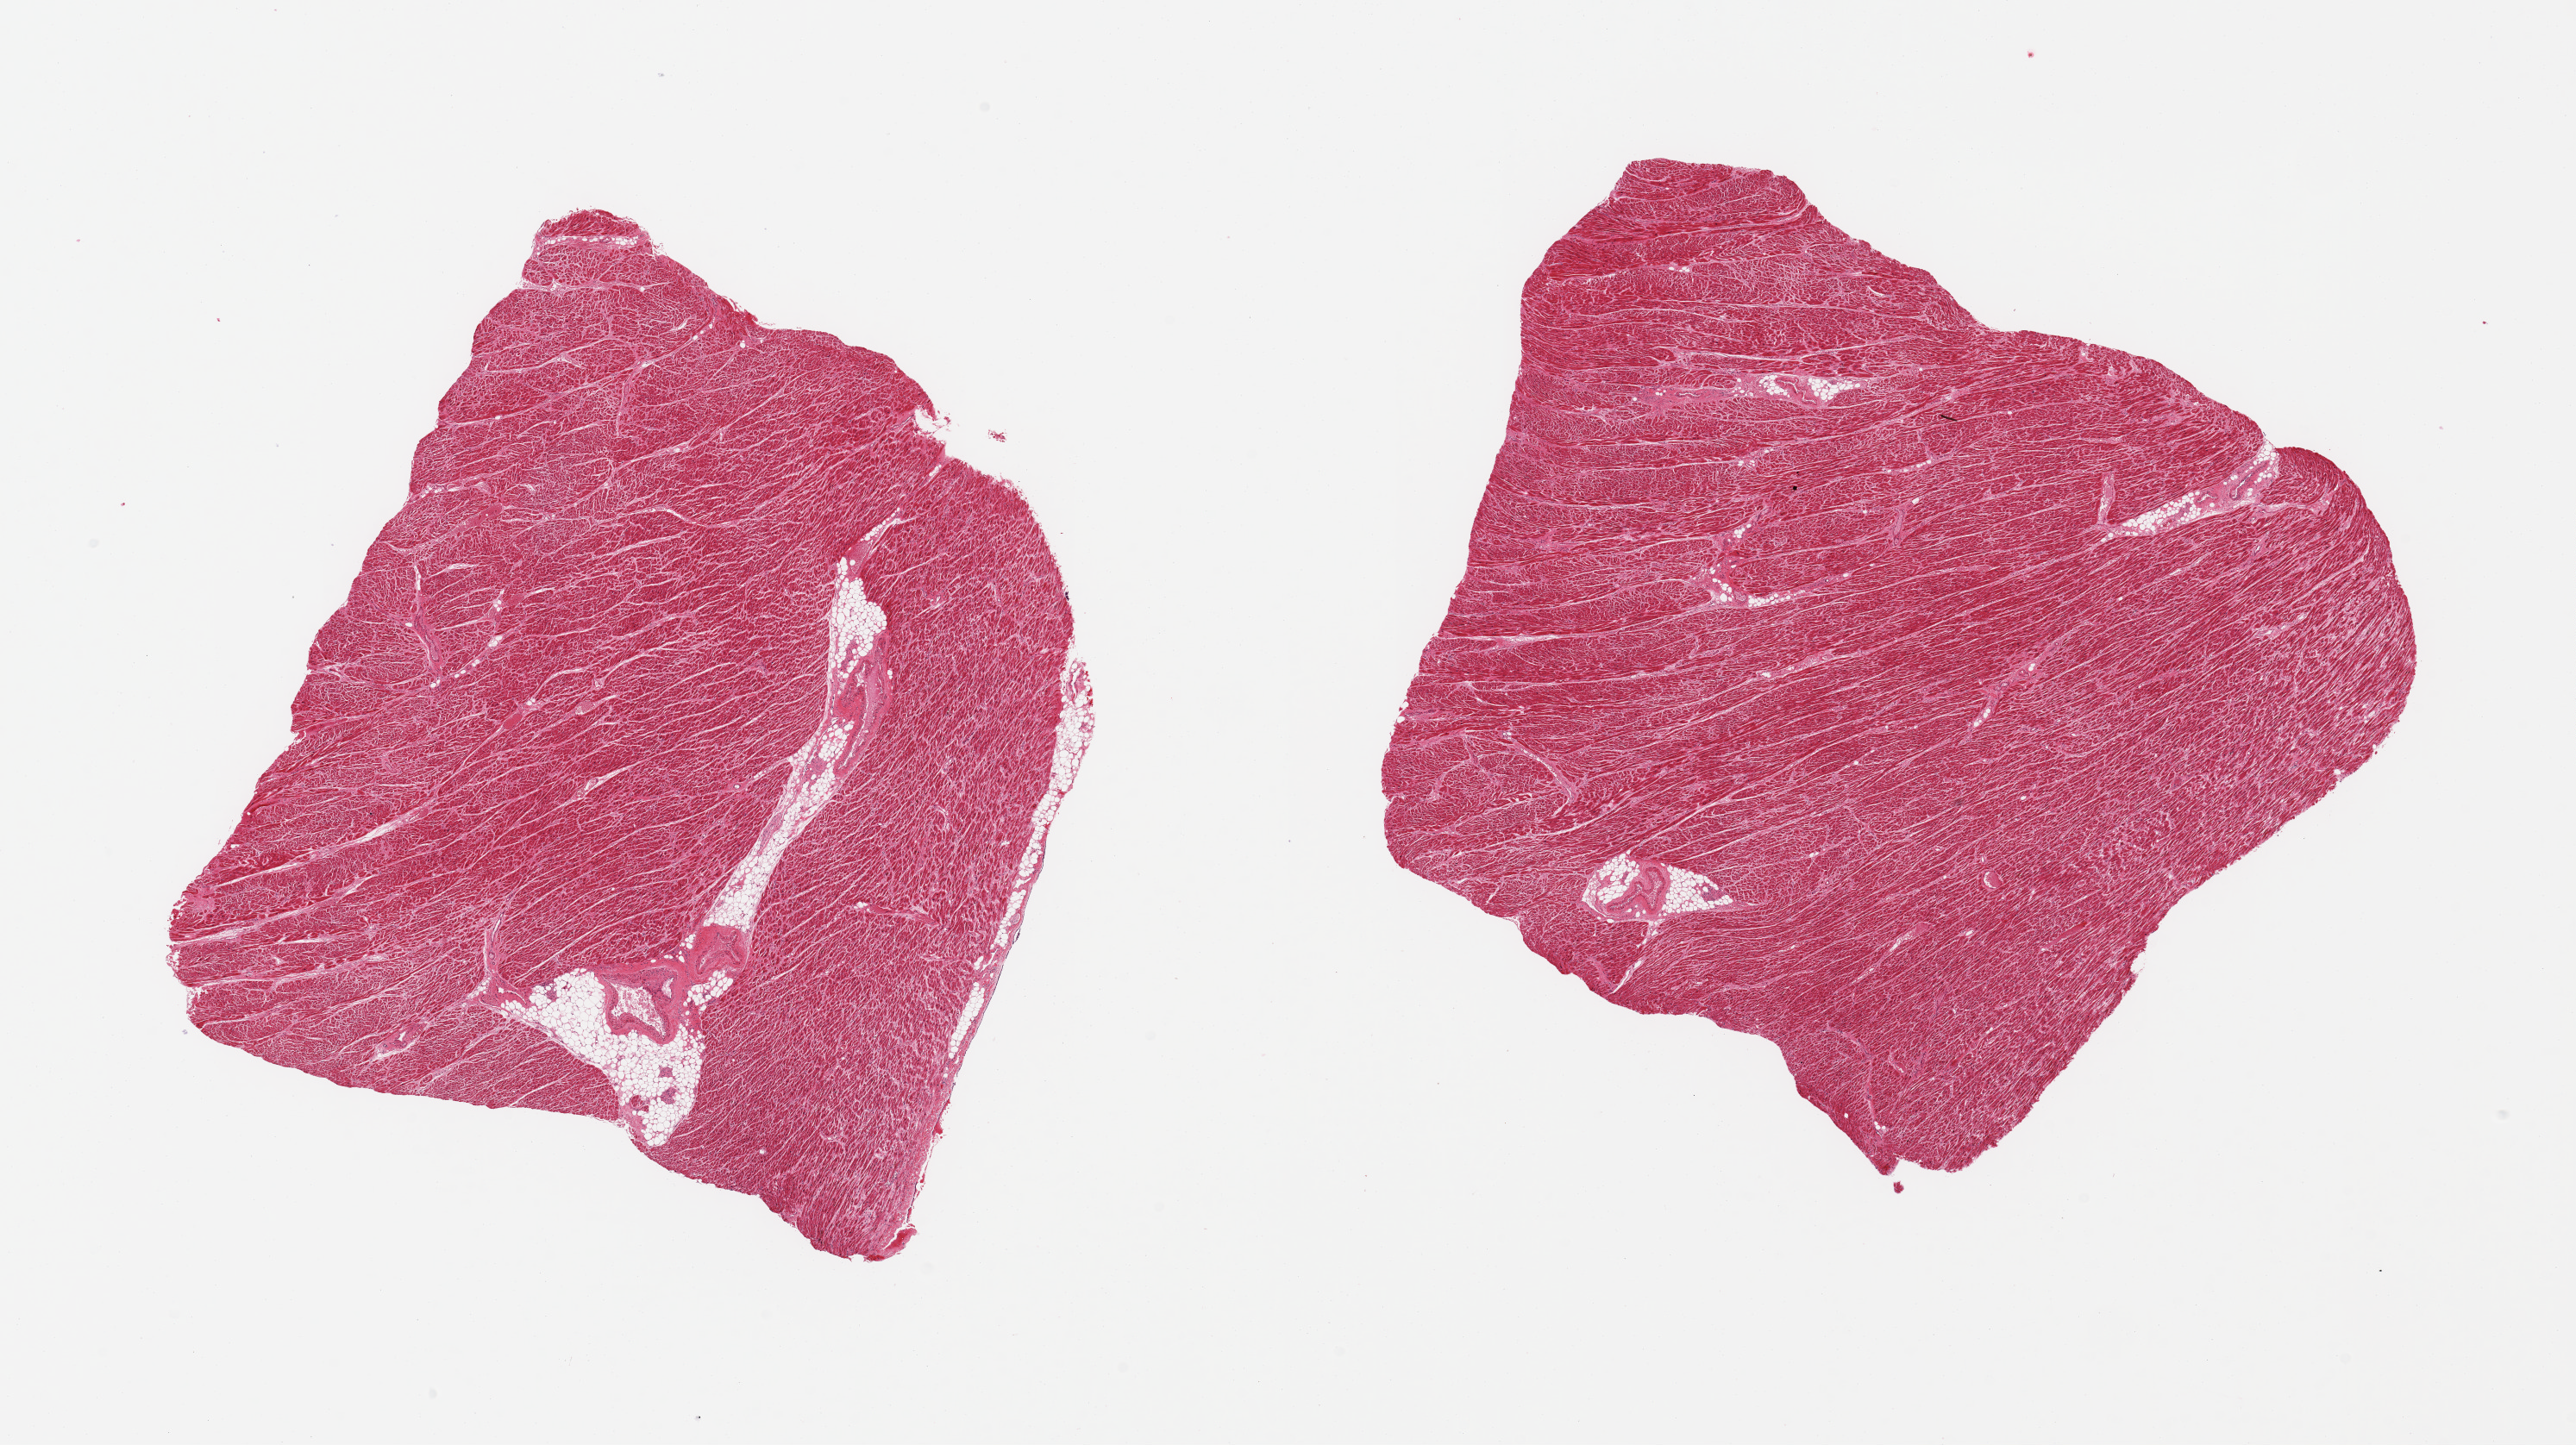
Hematoxylin and eosin (H&E) whole-slide image, brightfield, shown as a low-resolution overview of the whole scanned area (about 23.6 x 13.3 mm); PAXgene-fixed, paraffin-embedded tissue; target tissue: heart; donor tissue sample. Donor sex: female.
- pathologist's review note for this sample: 2 pieces; 5% internal fat